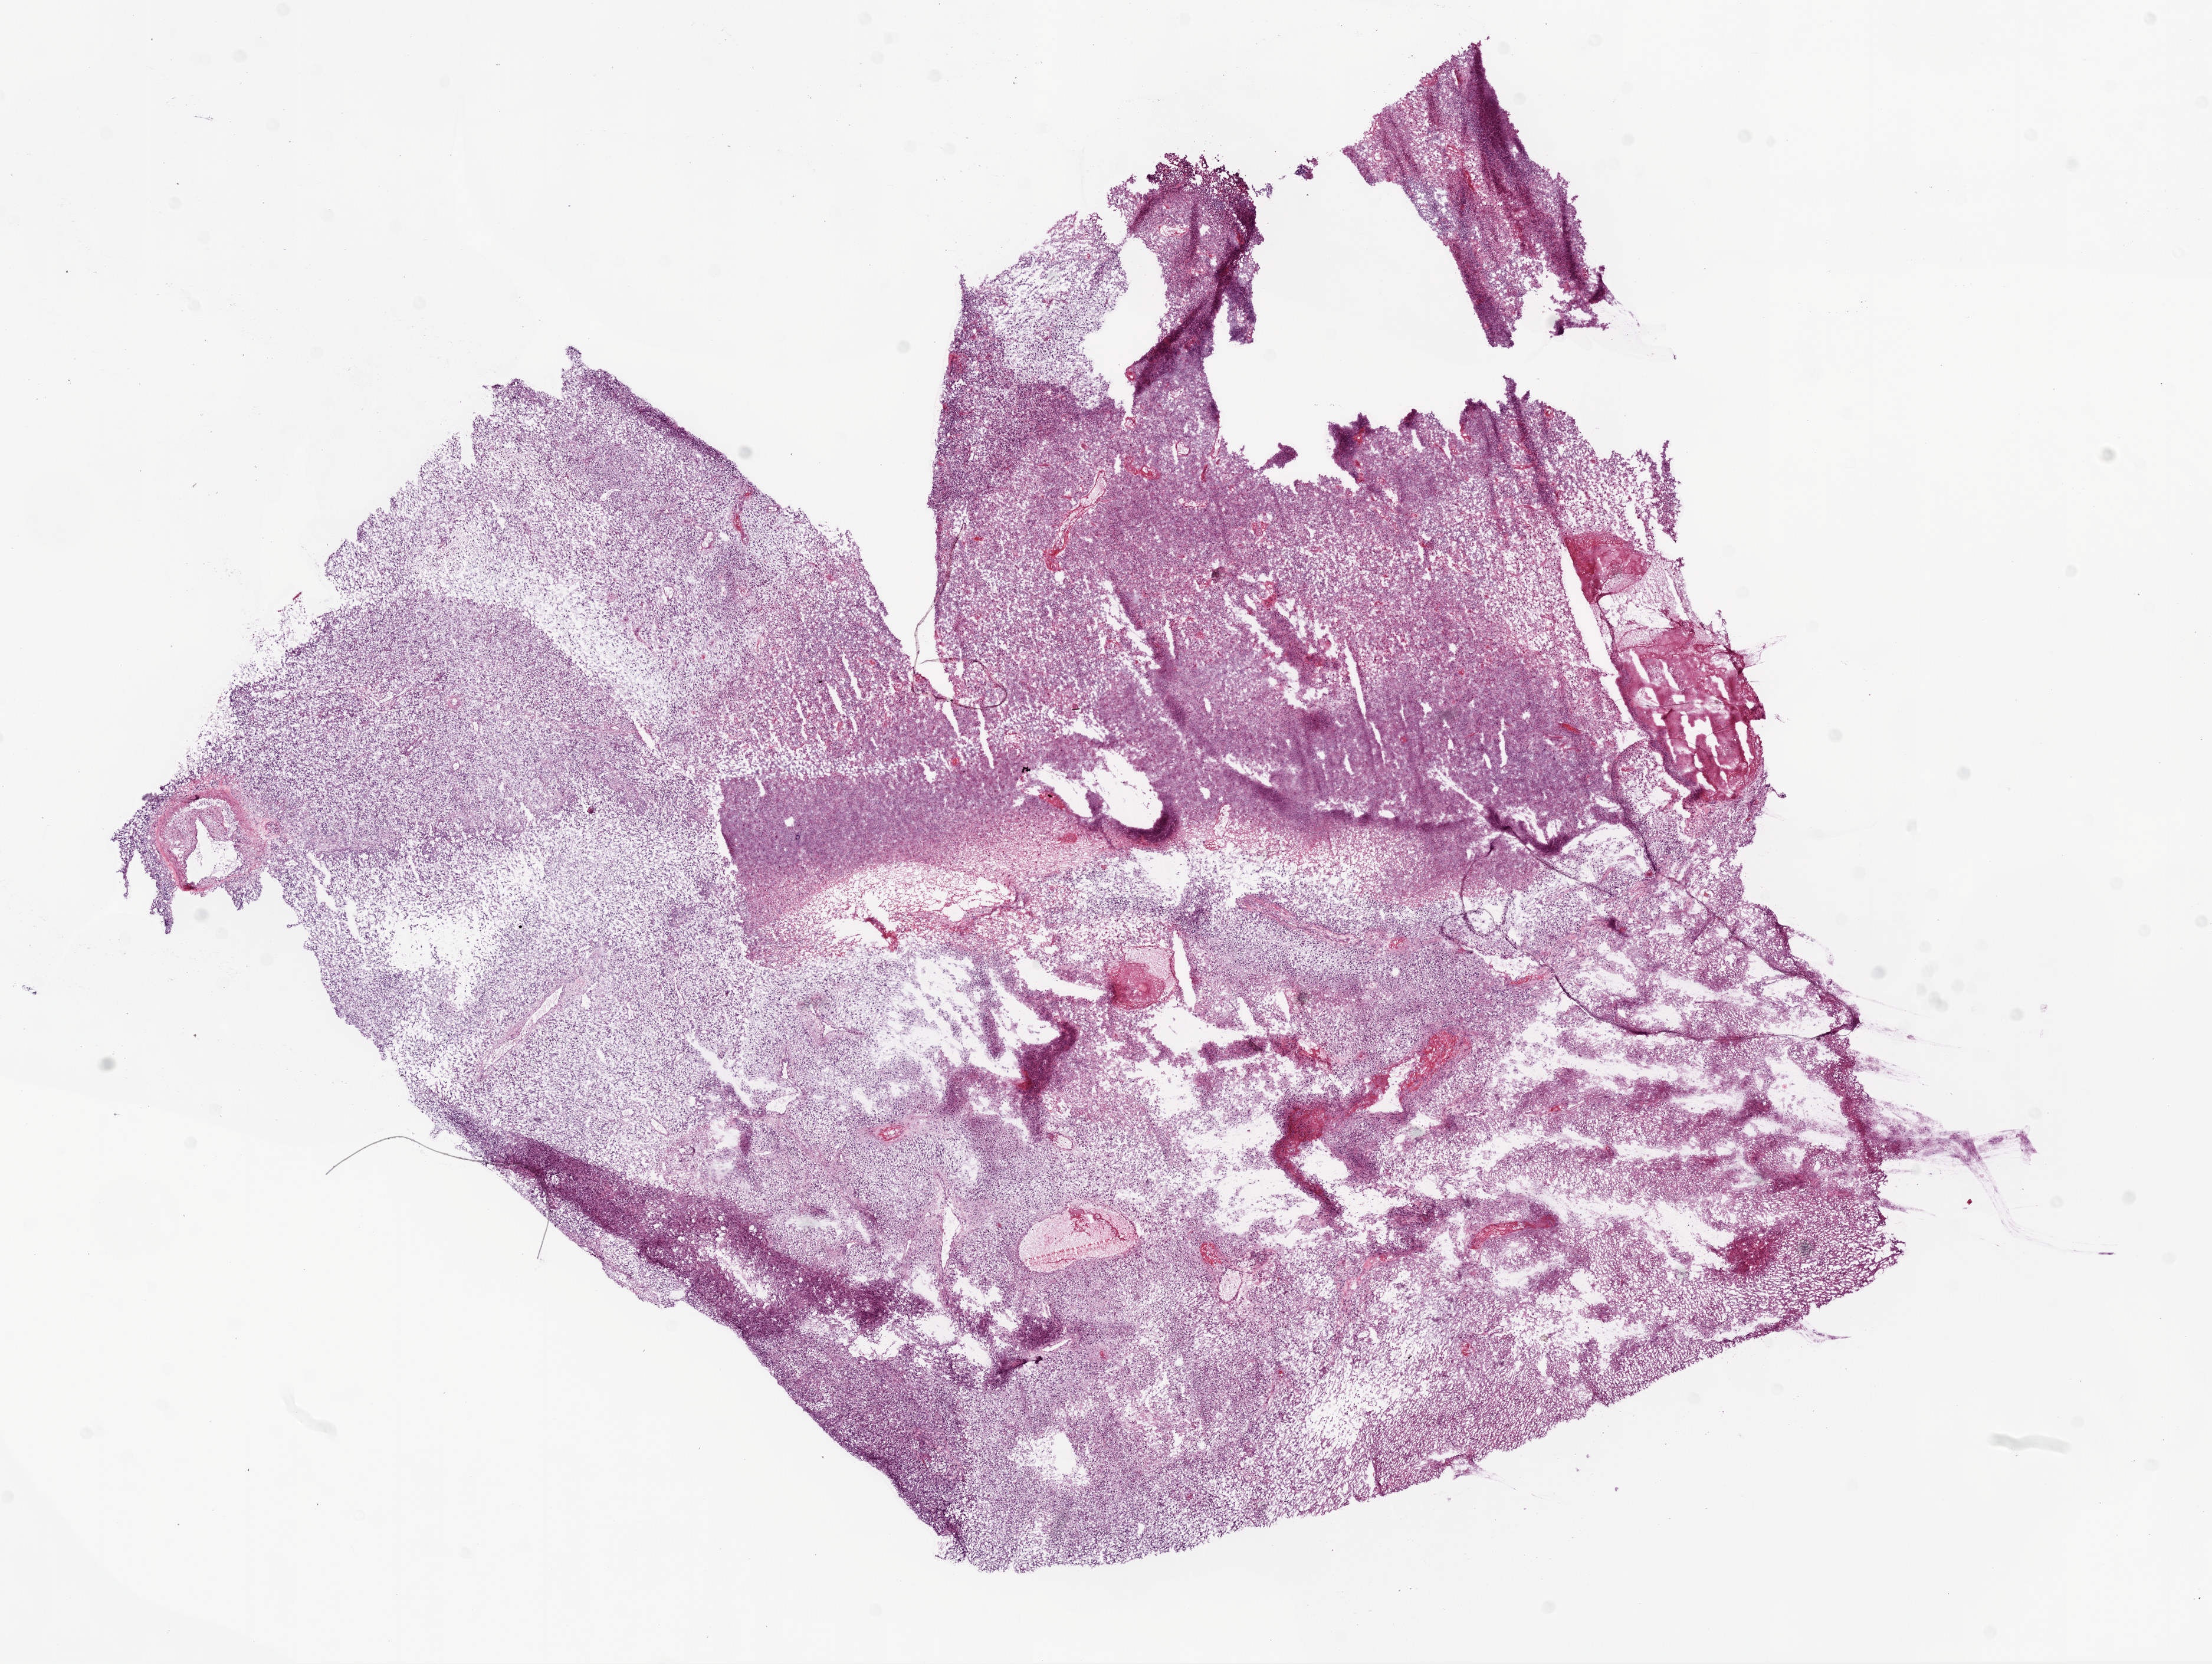
Whole-slide histology image, H&E, whole scanned area (about 15.0 x 11.3 mm, acquisition: 20x scan) shown as a low-resolution overview. Frozen section. Sample: primary tumour, brain. Patient: female, age at initial diagnosis 61 years. Pathologist review of this section (percent, as recorded): tumour cells 75%, tumour nuclei 90%, normal cells 5%, stromal cells 5%, necrosis 15%.
• pathologic diagnosis: Glioblastoma